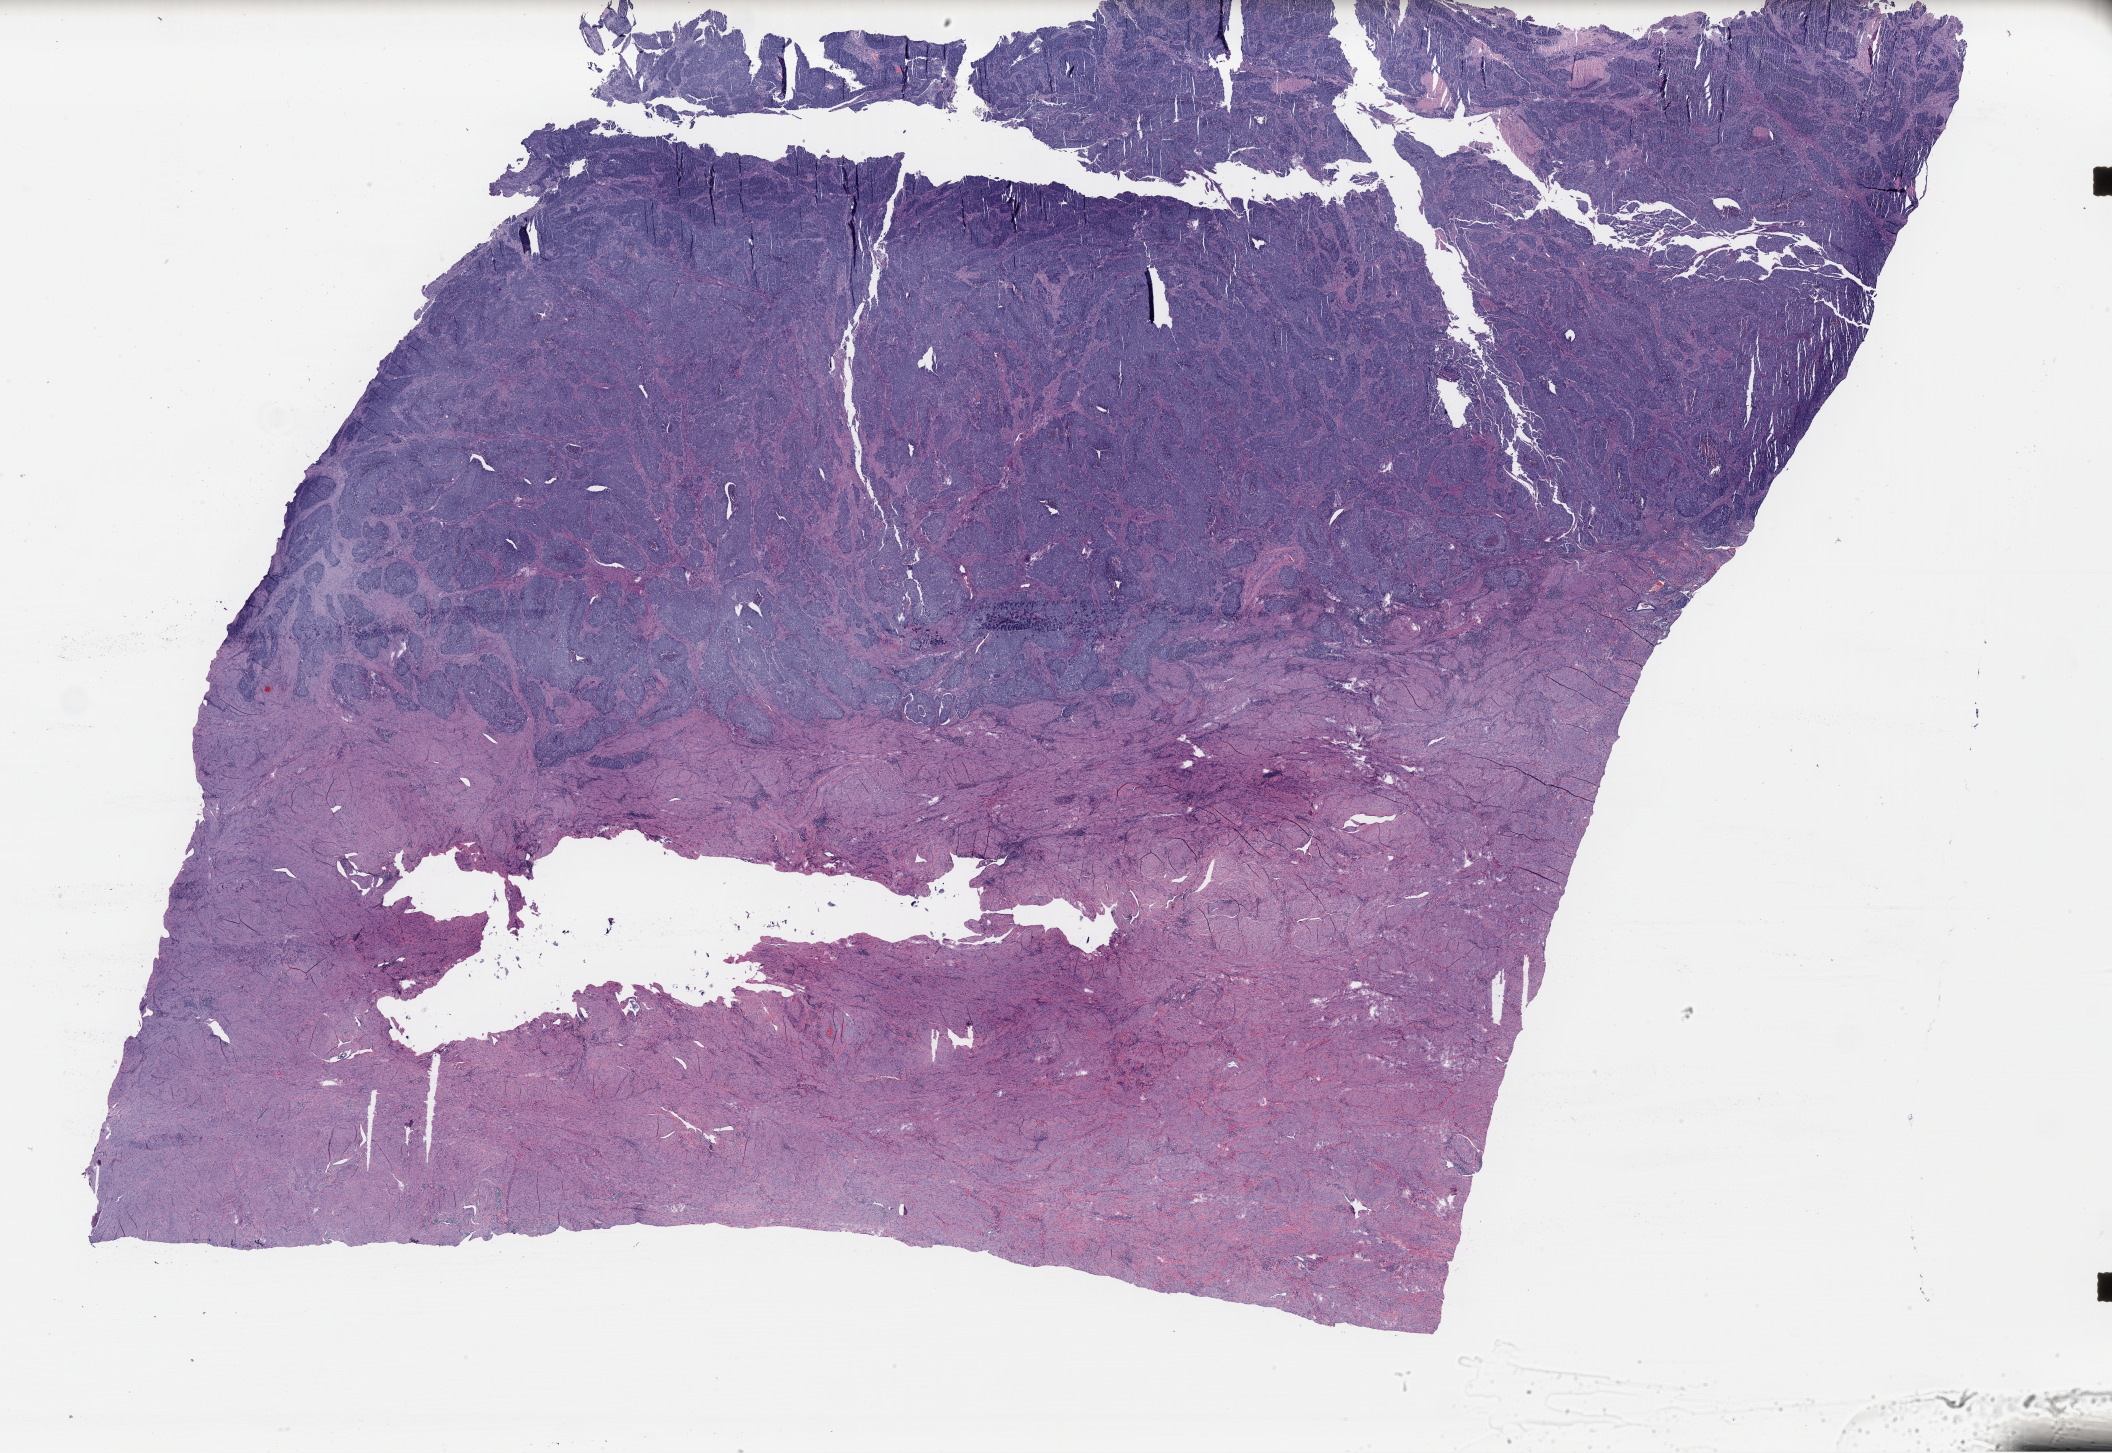
Whole-slide histology image, H&E, whole scanned area (about 33.4 x 23.0 mm) shown as a low-resolution overview; formalin-fixed paraffin-embedded (FFPE) diagnostic section; uterus, primary tumour sample. Female patient; age at initial diagnosis 49 years. Histologic grade: G3 (poorly differentiated).
* FIGO stage: IA
* diagnosis: Endometrioid adenocarcinoma, NOS